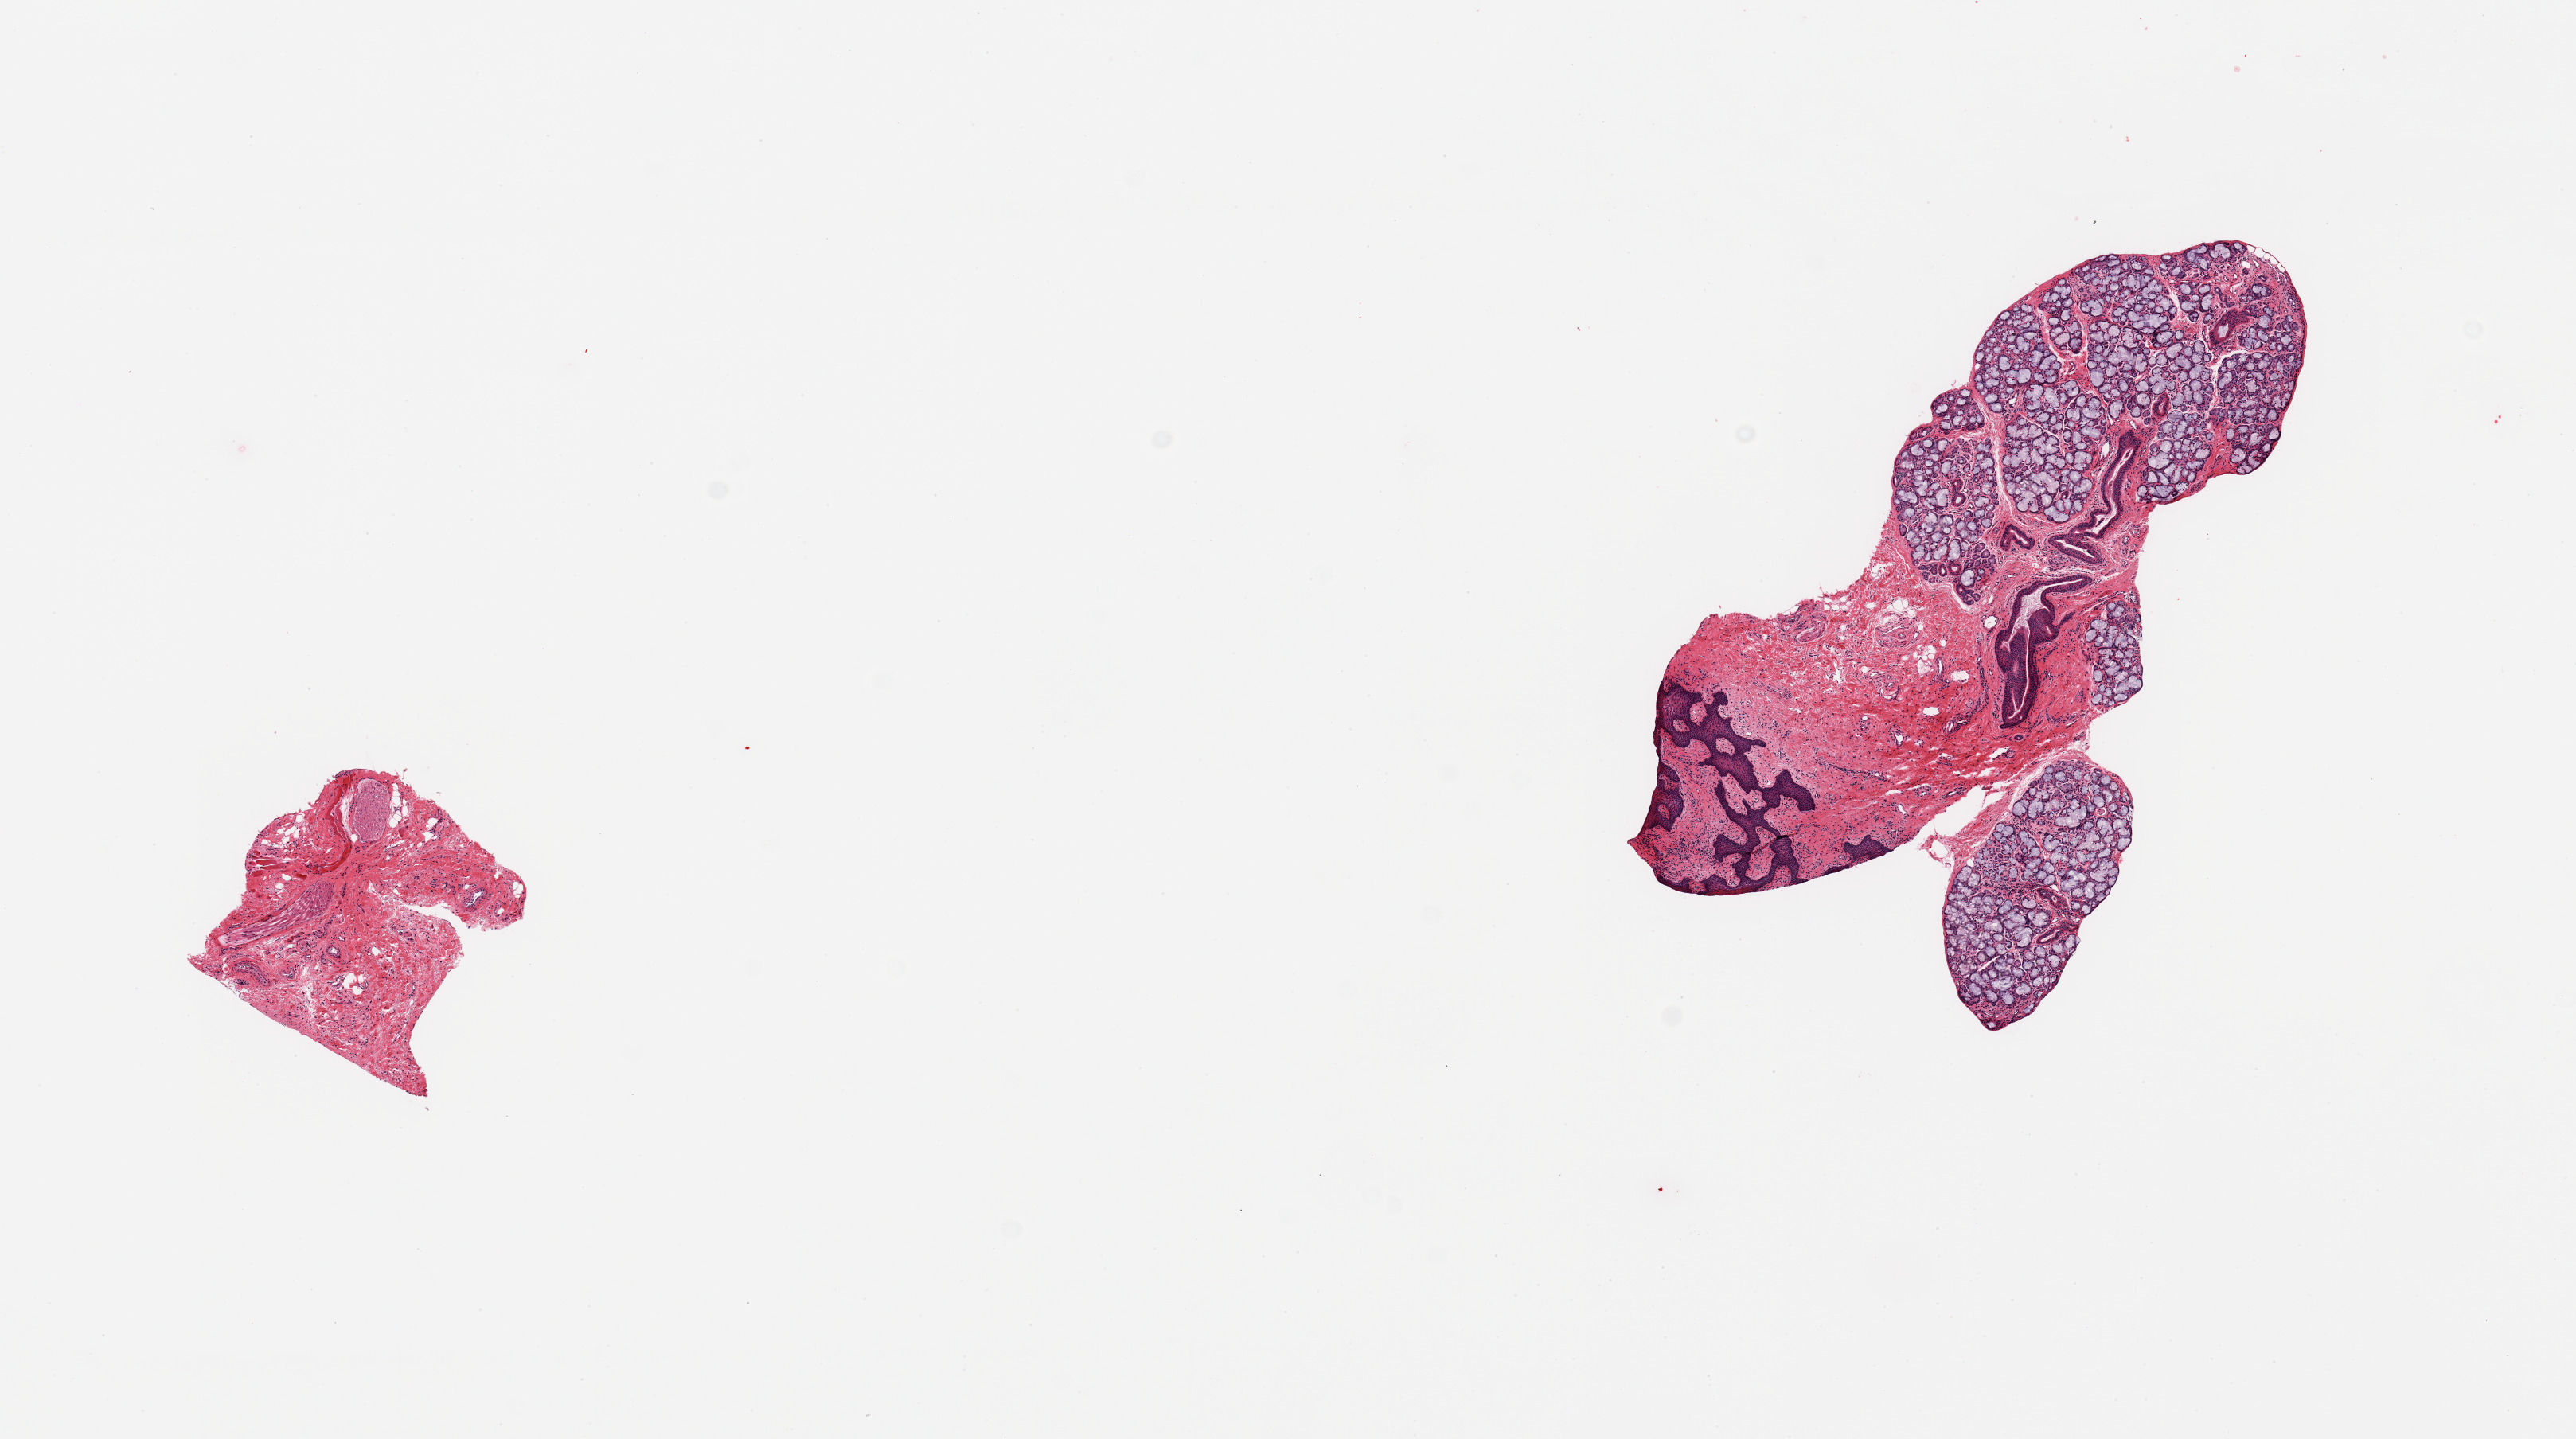
Whole-slide image, haematoxylin and eosin stain — whole scanned area (about 12.8 x 7.2 mm) shown as a low-resolution overview. PAXgene-fixed paraffin-embedded (PFPE) section. Section of minor salivary gland (target tissue). Tissue donor sample.
Pathologist's review note for this sample: 2 pieces; 1 piece contains 60% salivary glands and 40% fibrous stroma and squamous epithelium; smaller piece is all fibrous stroma [images].